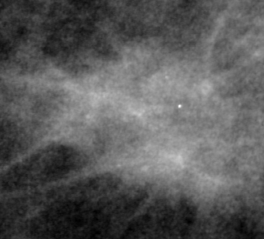
Region of interest cut from a scanned film mammogram (one marked finding); left breast; MLO view.
Mass, shape oval, margins spiculated; BI-RADS assessment category 4; subtlety rating 3 on a 1 (subtle) to 5 (obvious) scale; pathology result (as recorded, not read from the image): malignant.